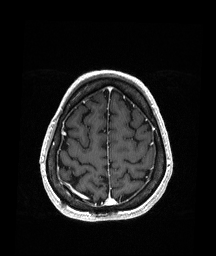
Brain MRI from a brain-tumour surgery series, one axial slice. Slice 51 of 151 in the series (ordered by position). T1-weighted post-contrast. 1.05 mm slice thickness. 216 × 256 image matrix, field of view 211 × 250 mm. Case-level facts recorded for this patient, not image findings: histopathology: Oligodendroglioma; WHO grade: 2; IDH mutation: yes; tumour location: Right Parietal.
Structures marked on this image (outlined manually by an expert reader):
- previous resection cavity: bounding box (x1, y1, x2, y2) in pixels: (103, 176, 109, 182)